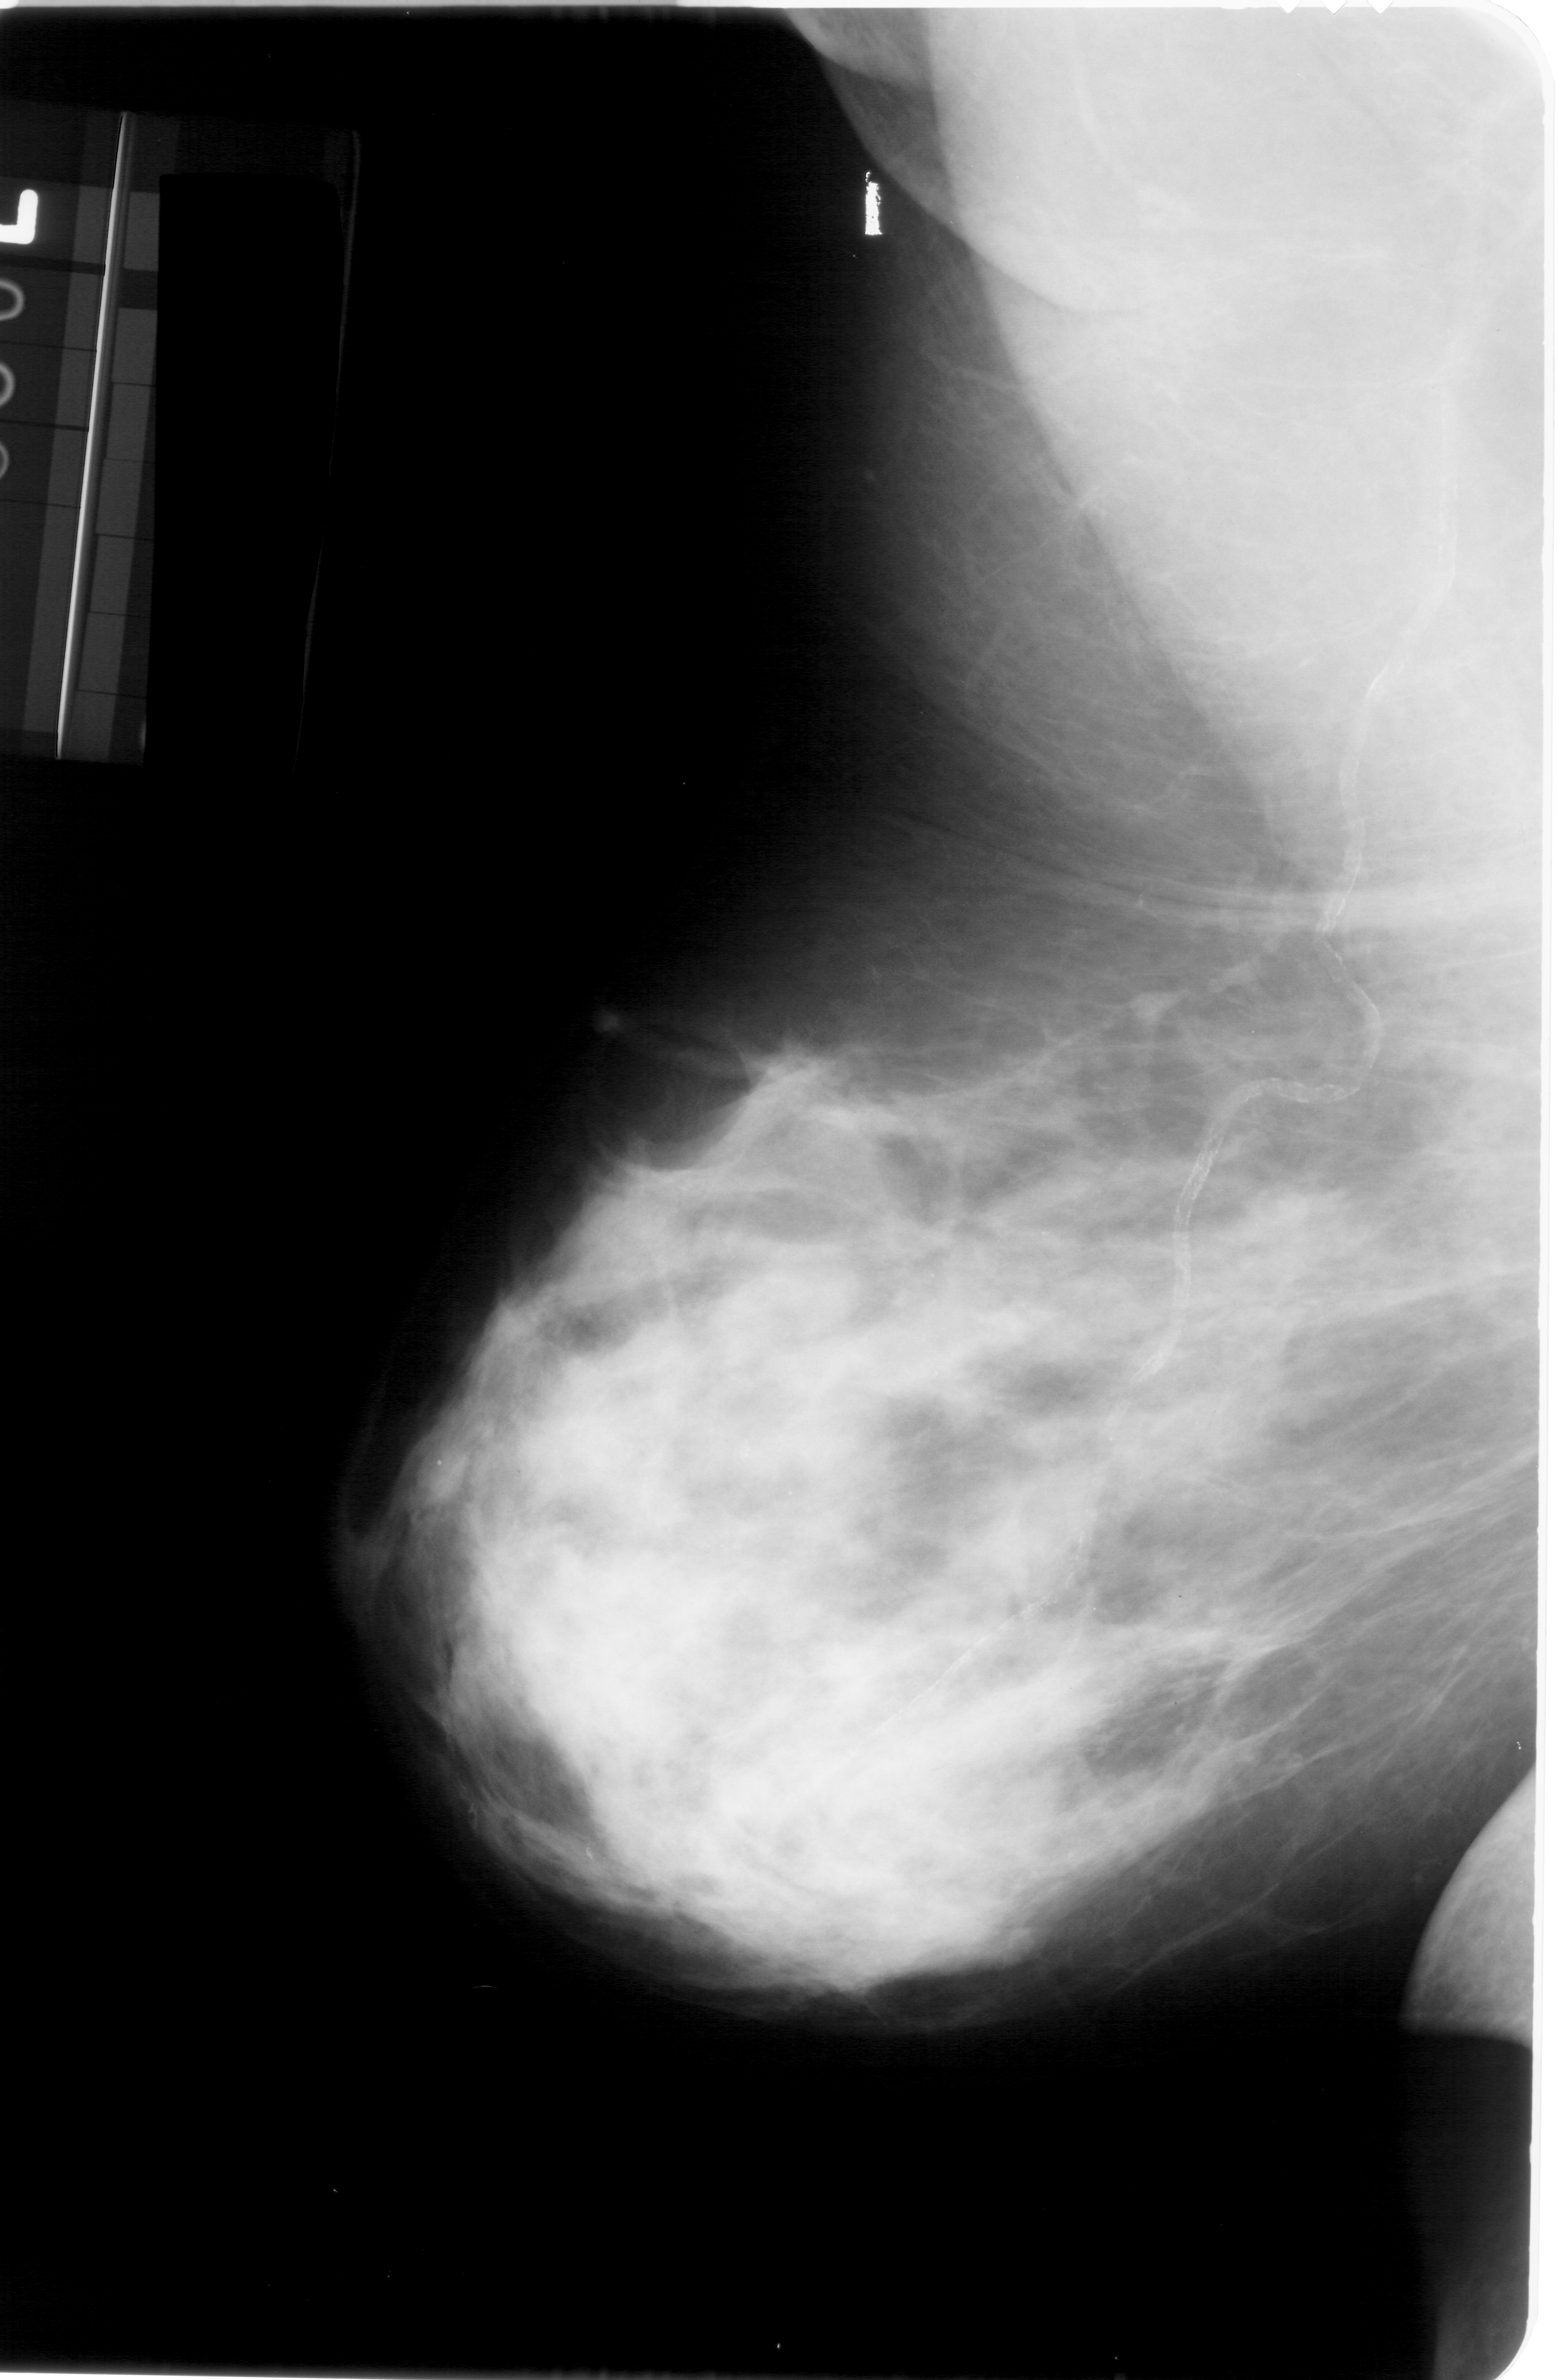
Mammogram (digitized film); left breast; MLO view; BI-RADS breast density category 4 (scale 1–4); 1558 × 2380 image matrix.
Expert-marked regions of interest on this film, with their recorded descriptors:
- calcifications, morphology pleomorphic, distribution segmental; BI-RADS assessment category 4; pathology (as recorded): malignant: bounding box (x1, y1, x2, y2) in pixels: (708, 1189, 1084, 1519)